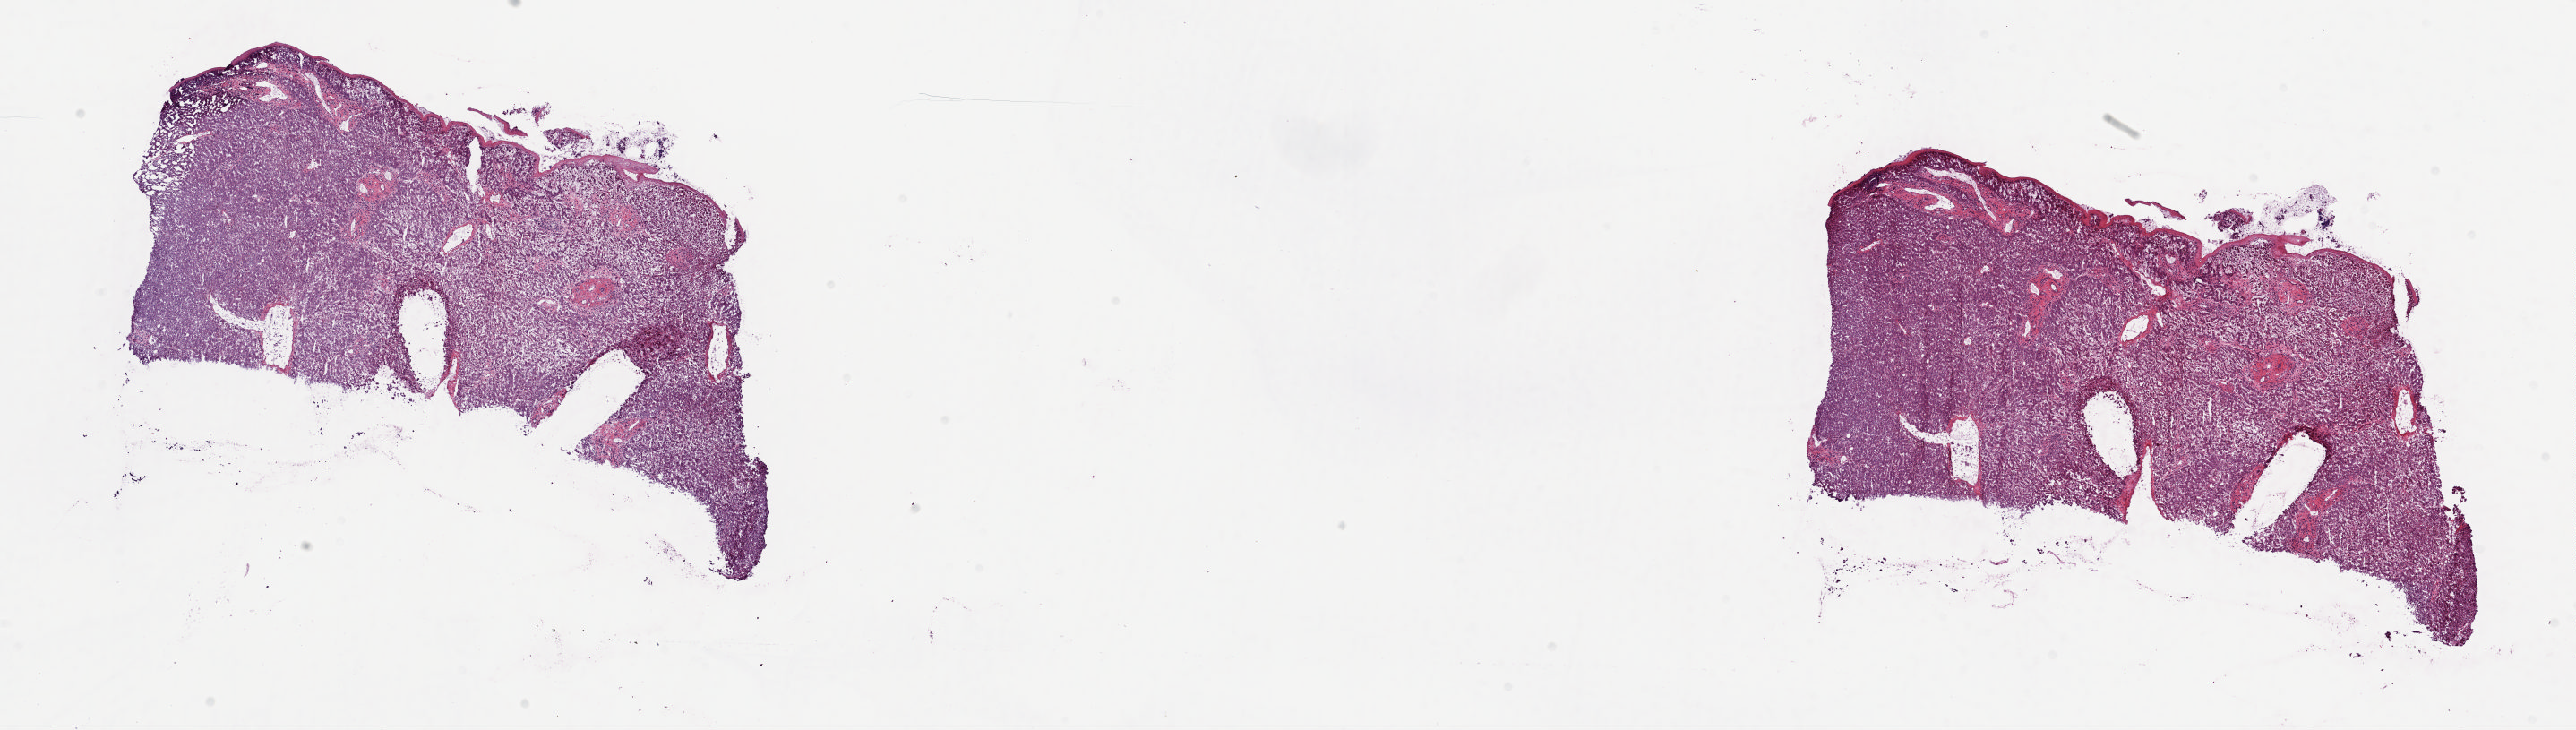
H&E whole-slide image — shown as a low-resolution overview of the whole scanned area (about 22.8 x 6.5 mm); frozen section from the top of the tissue portion; bile duct, solid tissue normal (non-tumour tissue) sample. Male patient; age at initial diagnosis 57 years. Slide review estimates, as recorded: tumour cells 0%, tumour nuclei 0%, normal cells 80%, stromal cells 20%, necrosis 0%. Inflammatory infiltration, as recorded: lymphocyte infiltration 3%, monocyte infiltration 1%, neutrophil infiltration 2%.
• this section: solid tissue normal (non-tumour) sample from the same patient
• patient diagnosis: Cholangiocarcinoma (intrahepatic bile duct)